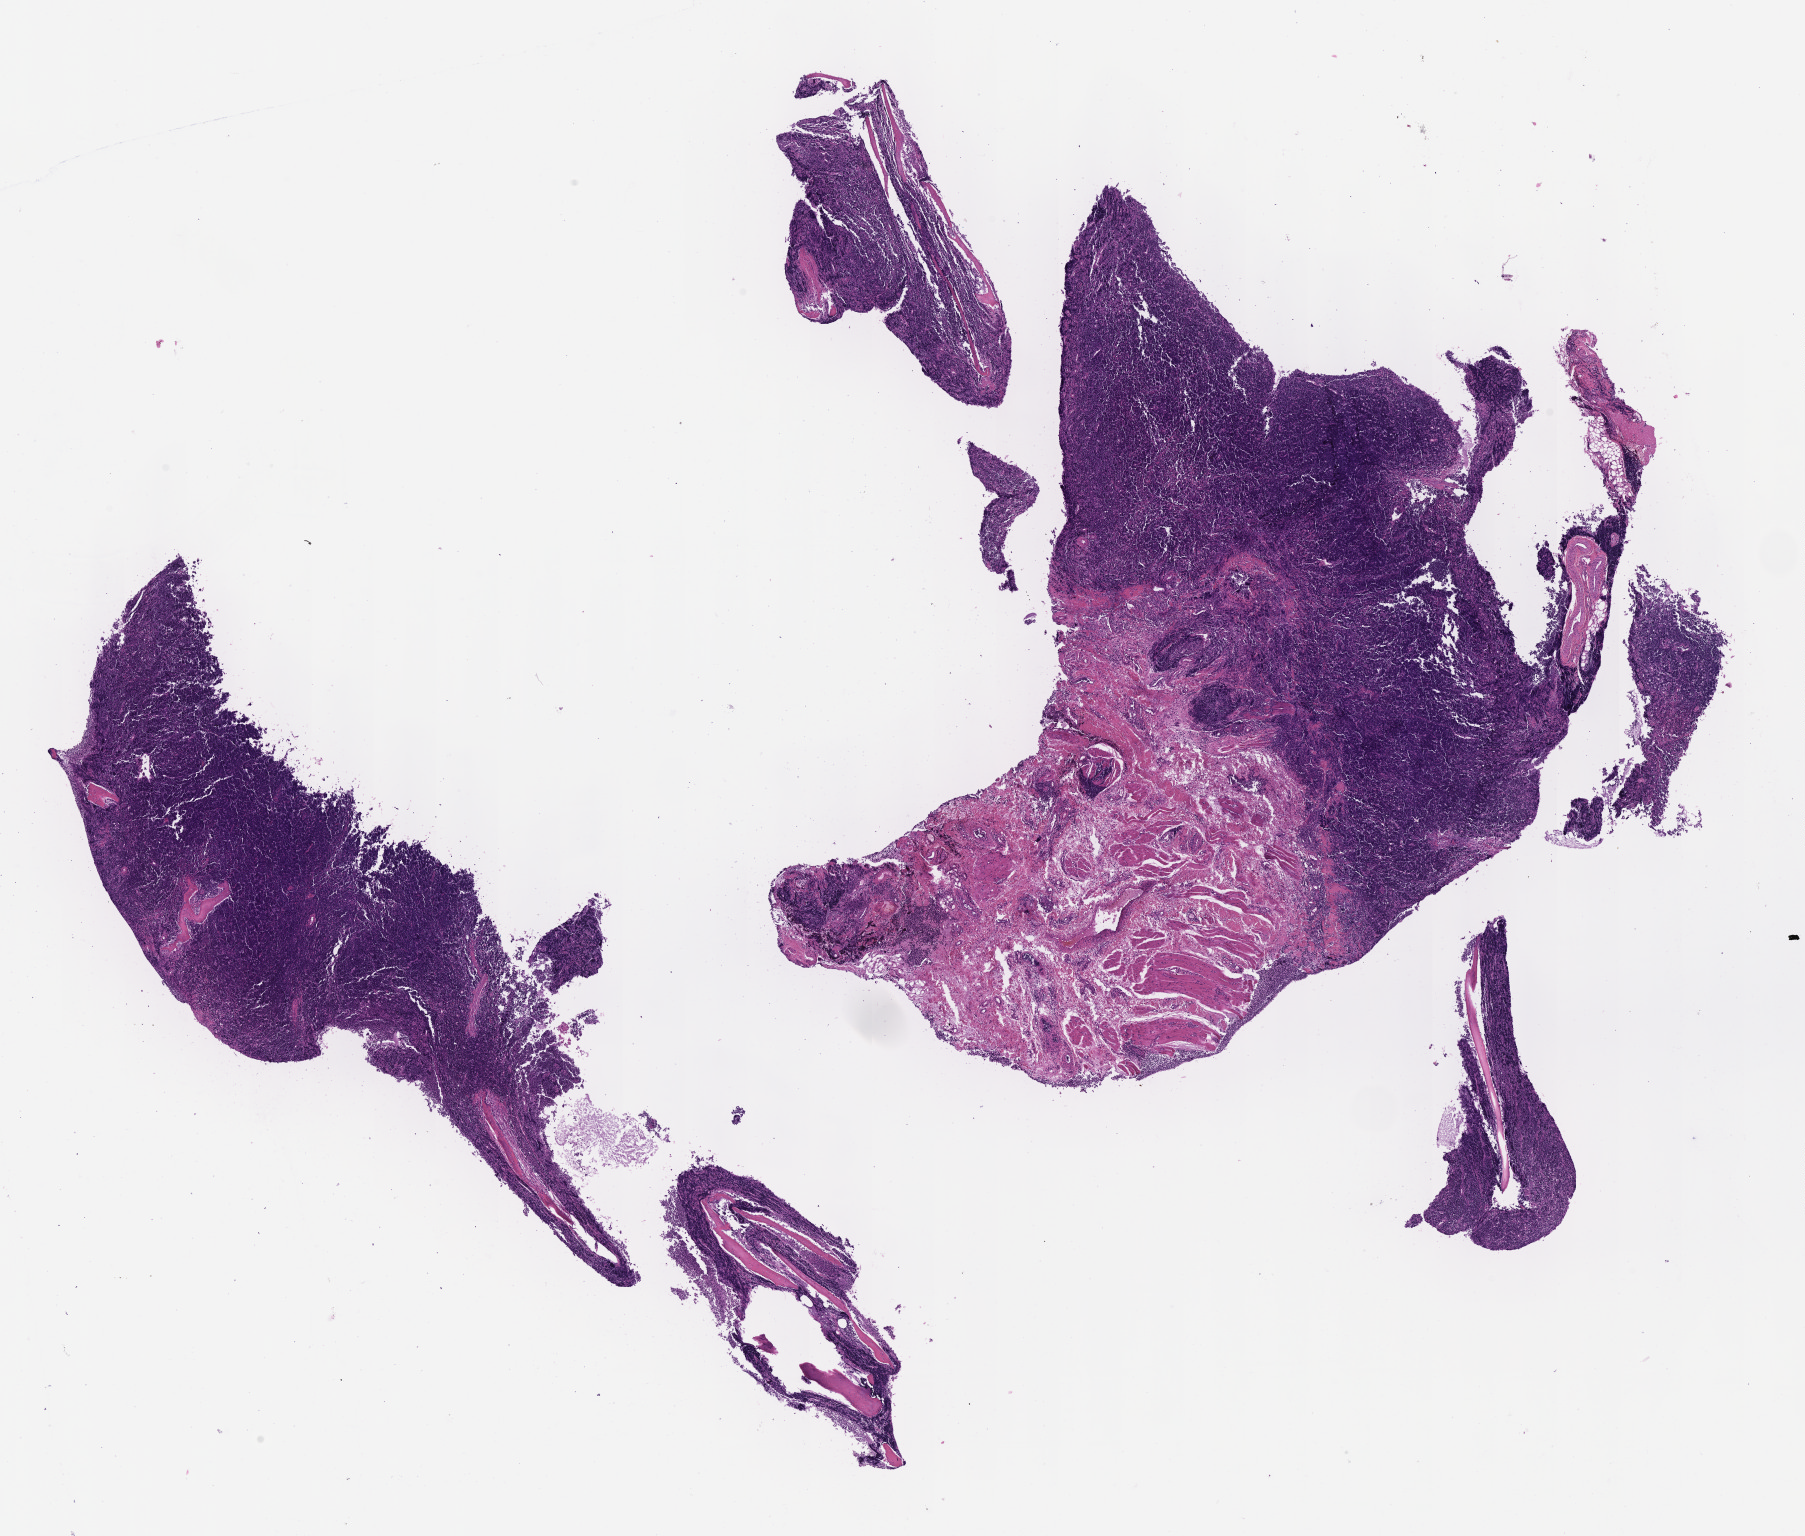
Digitized hematoxylin and eosin (H&E)-stained section, a low-resolution overview of the entire scanned area, about 14.6 x 12.4 mm. Specimen: tumor tissue. Anatomic site: cranium. Patient: male, age at initial diagnosis 8 years.
Diagnosis: Burkitt lymphoma, NOS.